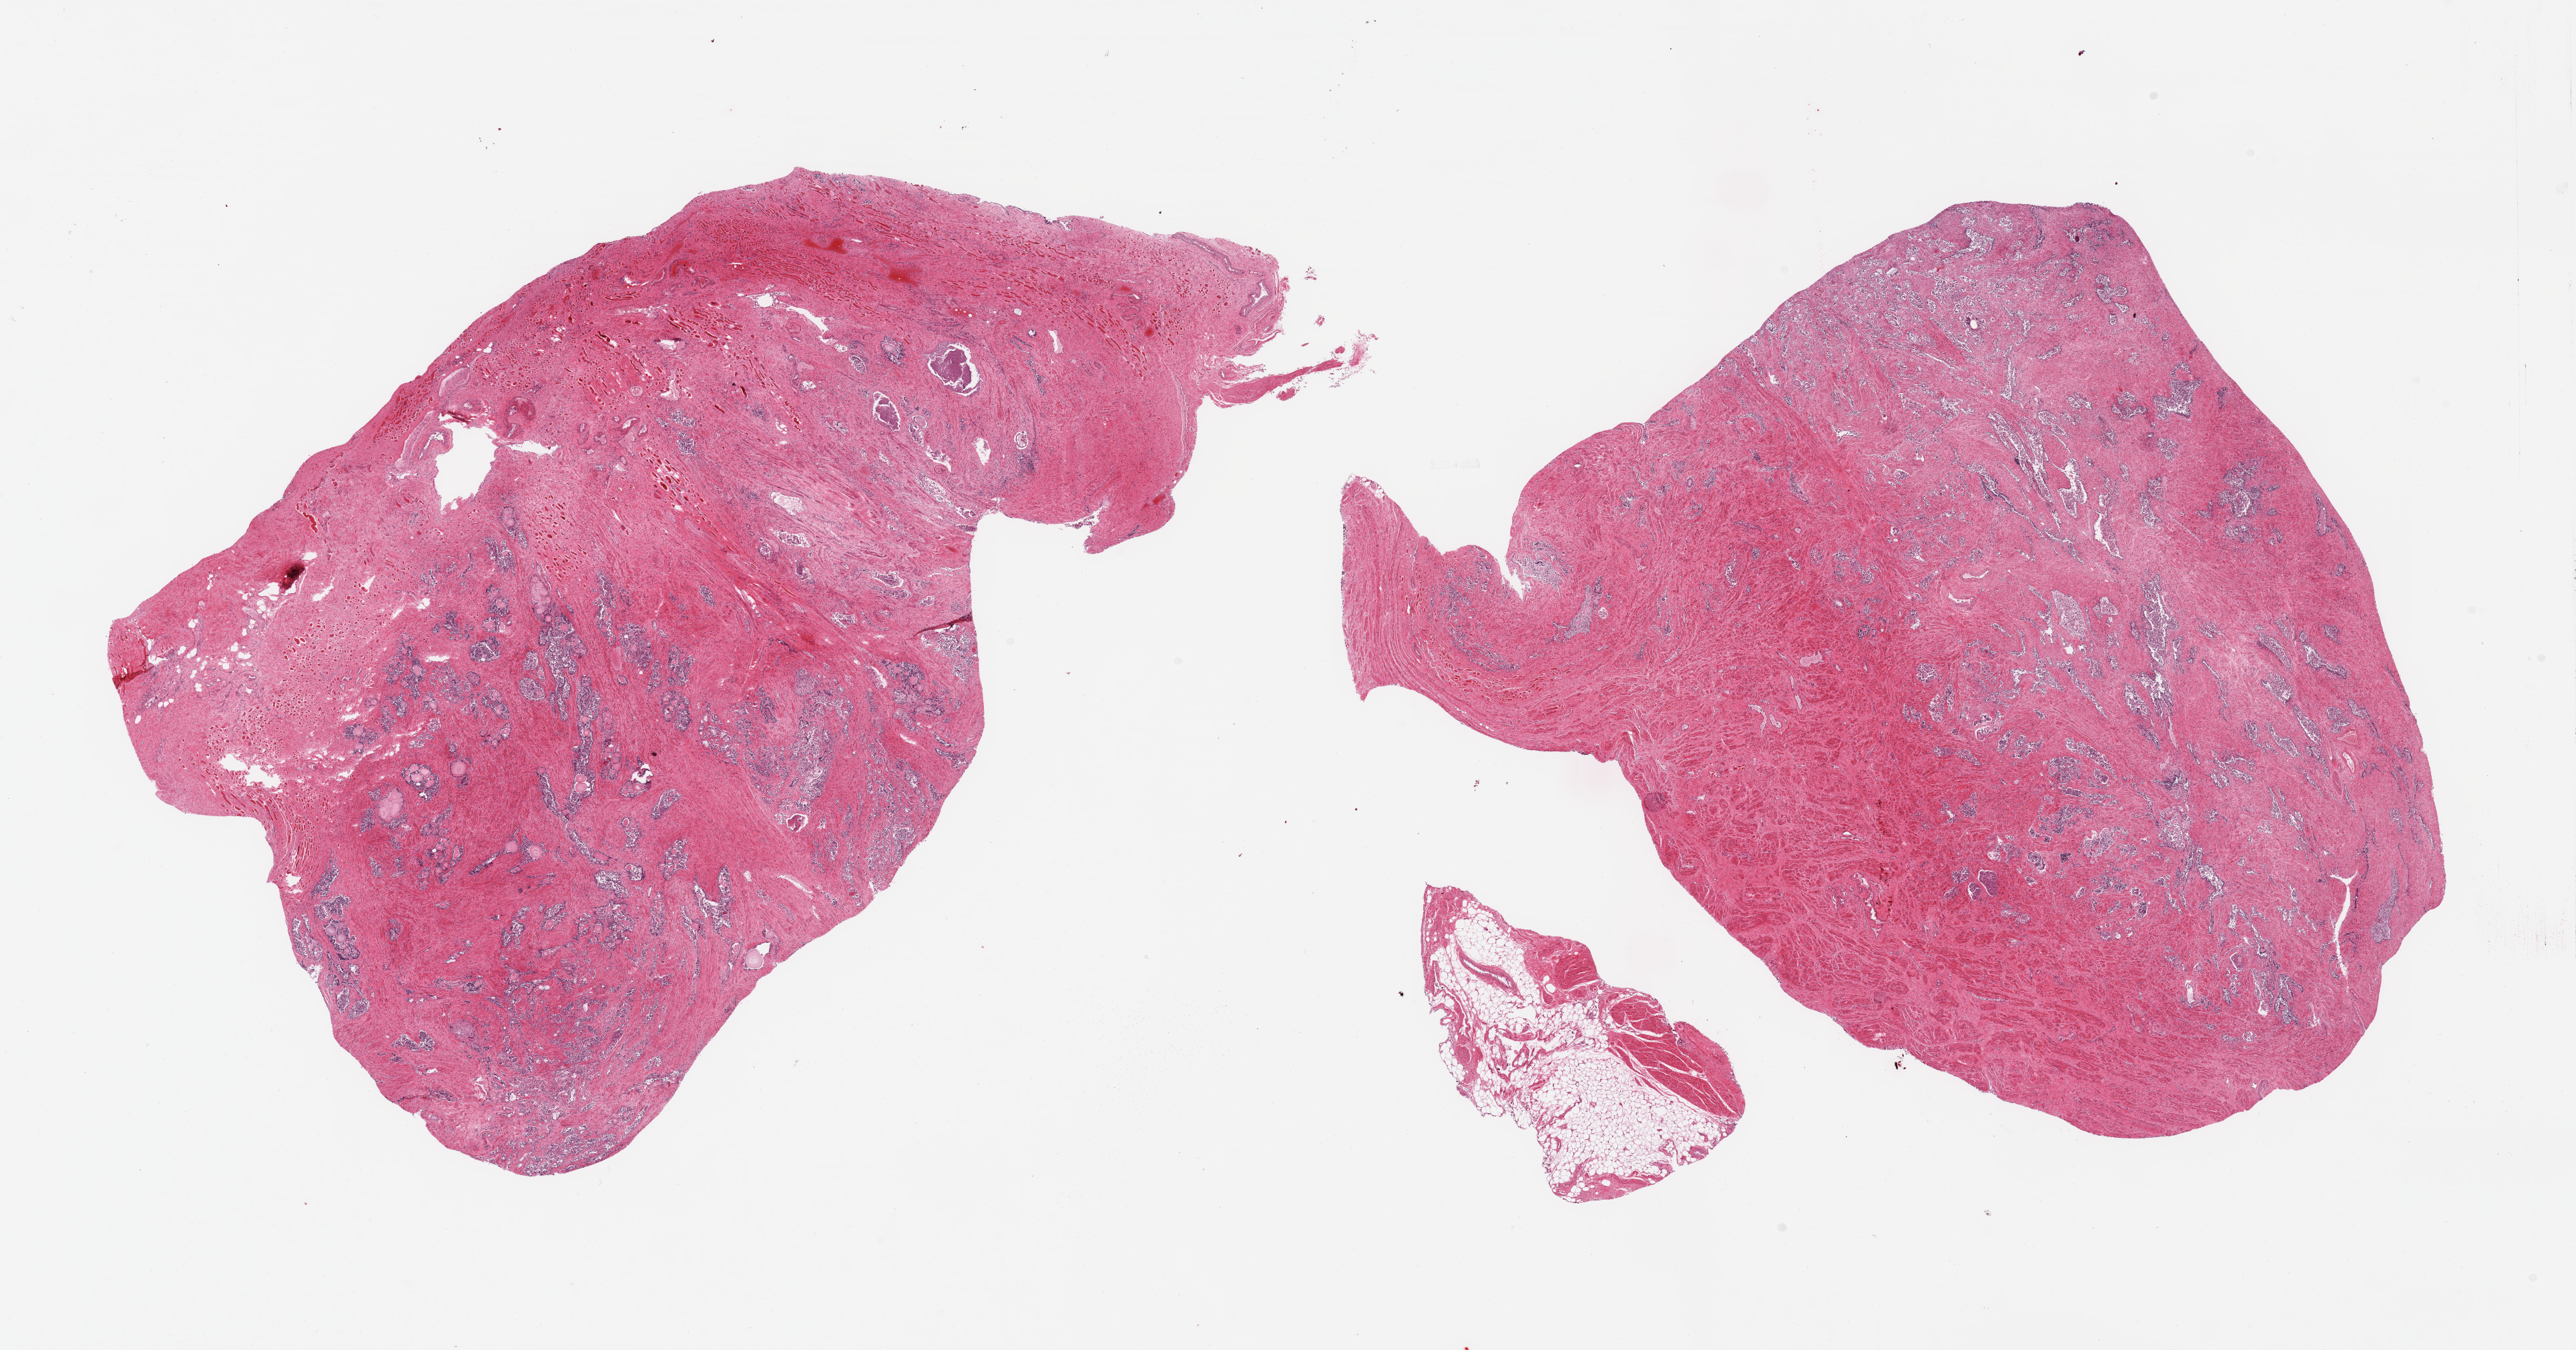
Digitized hematoxylin and eosin (H&E)-stained section, a low-resolution overview of the entire scanned area, about 30.5 x 16.0 mm (from a 20x scan). PAXgene-fixed, paraffin-embedded tissue. Section of prostate (target tissue). Donor tissue sample. Male donor.
• review note (as recorded): 2 pieces, hyperplastic glandular pattern with moderately advanced mucosal autolysis